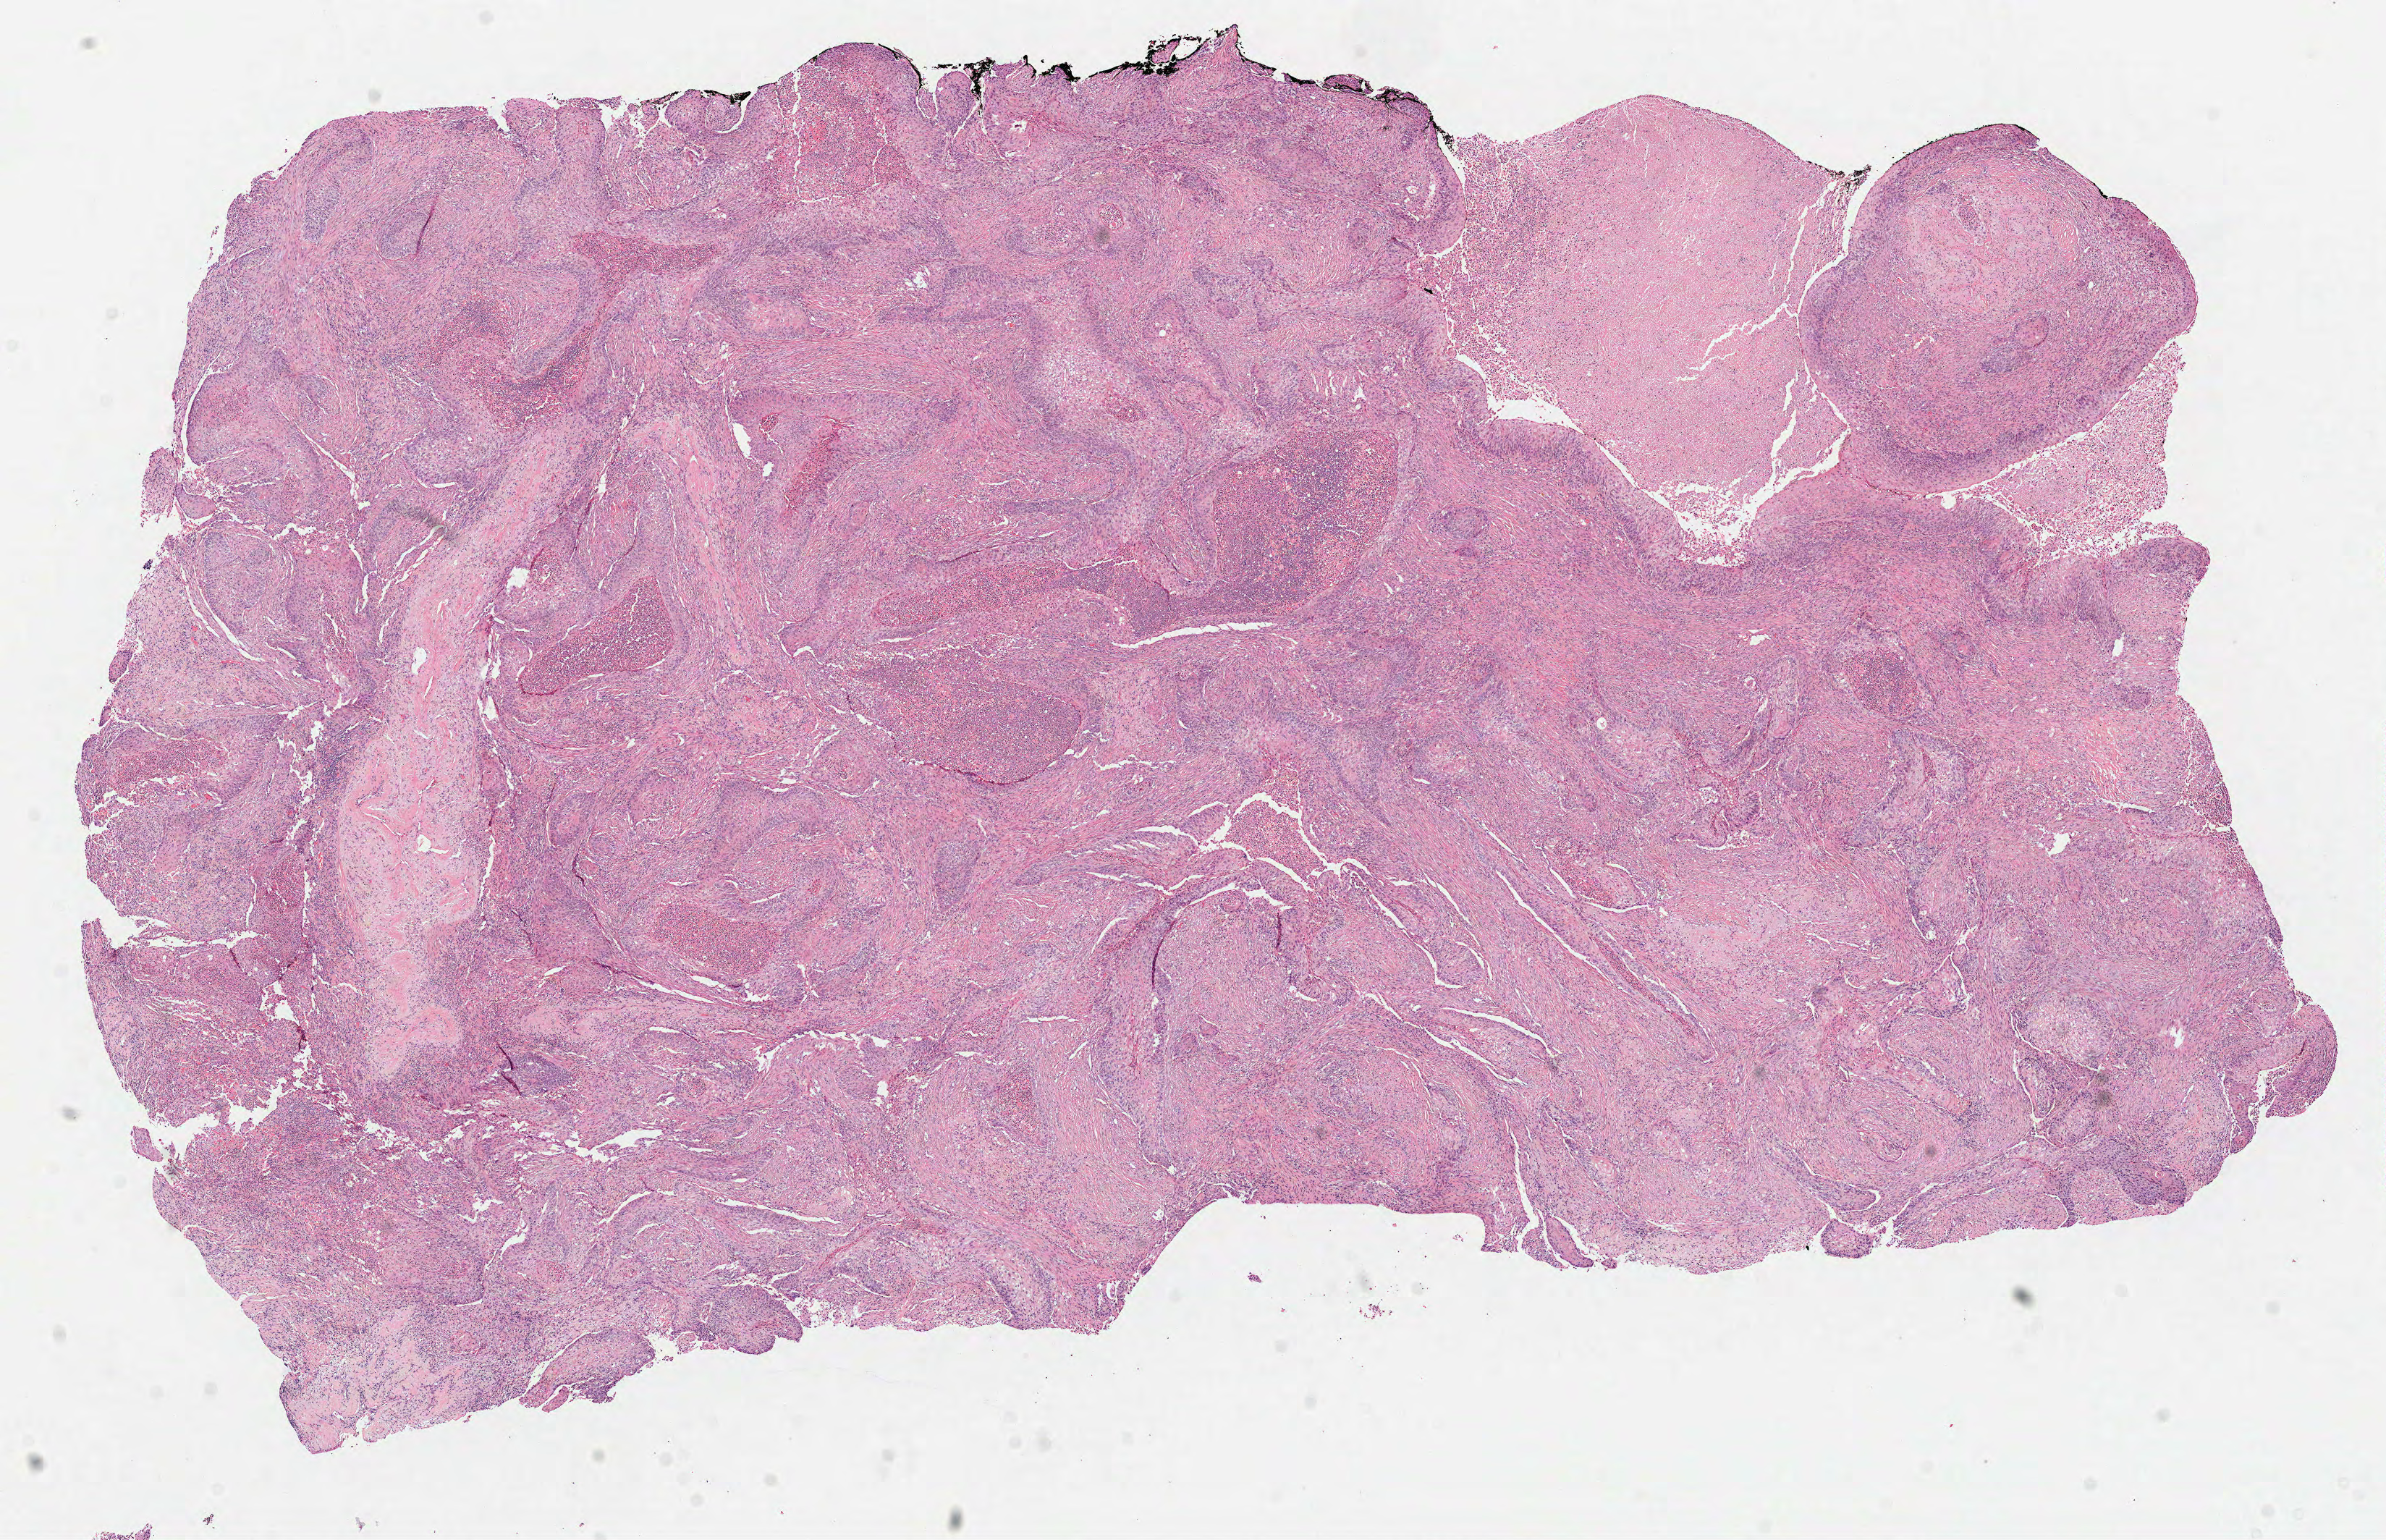
H&E-stained whole-slide image — whole scanned area (about 13.3 x 8.6 mm, from a 40x scan) shown as a low-resolution overview, formalin-fixed paraffin-embedded (FFPE) diagnostic section, primary tumour sample from the lung. Female patient; age at initial diagnosis 76 years.
Pathologic diagnosis: Squamous cell carcinoma, NOS (lower lobe, lung). AJCC pathologic stage: IIB (7th edition).